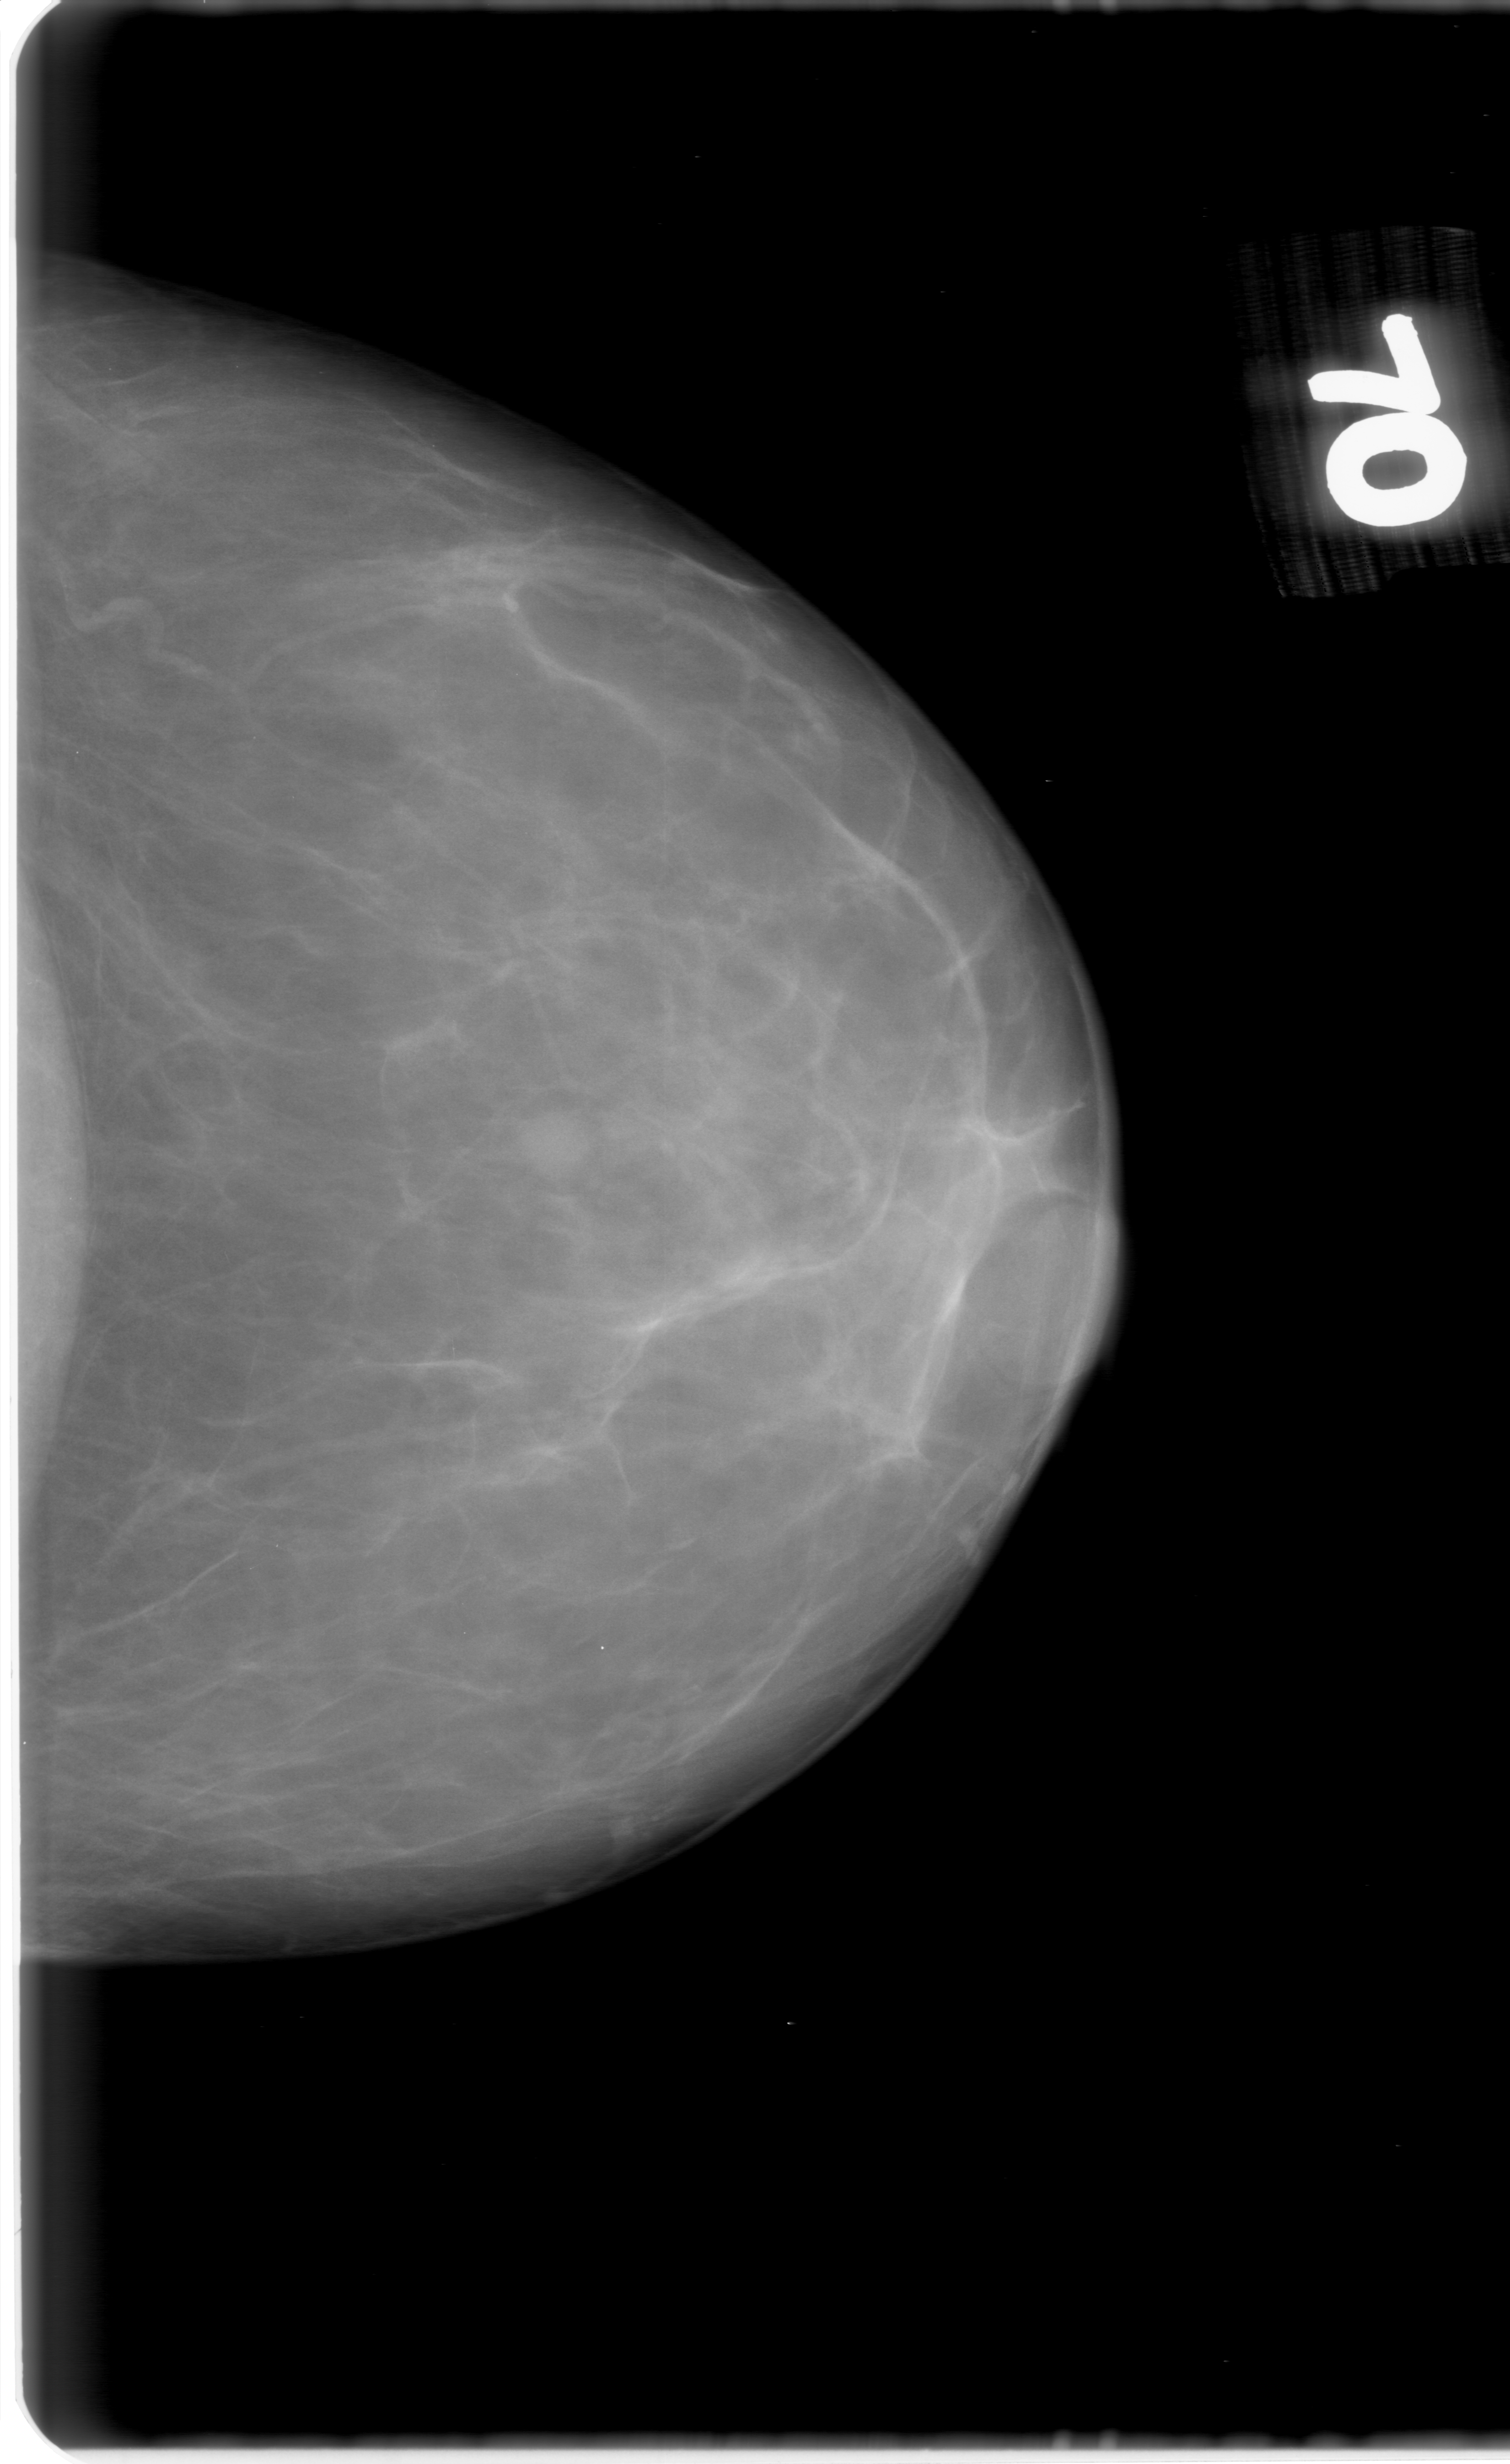
Scanned film-screen mammogram, left breast, craniocaudal (CC) view.
Finding: mass, shape round, margins obscured; BI-RADS assessment category 0 (incomplete: needs additional imaging); pathology result (as recorded, not read from the image): benign.